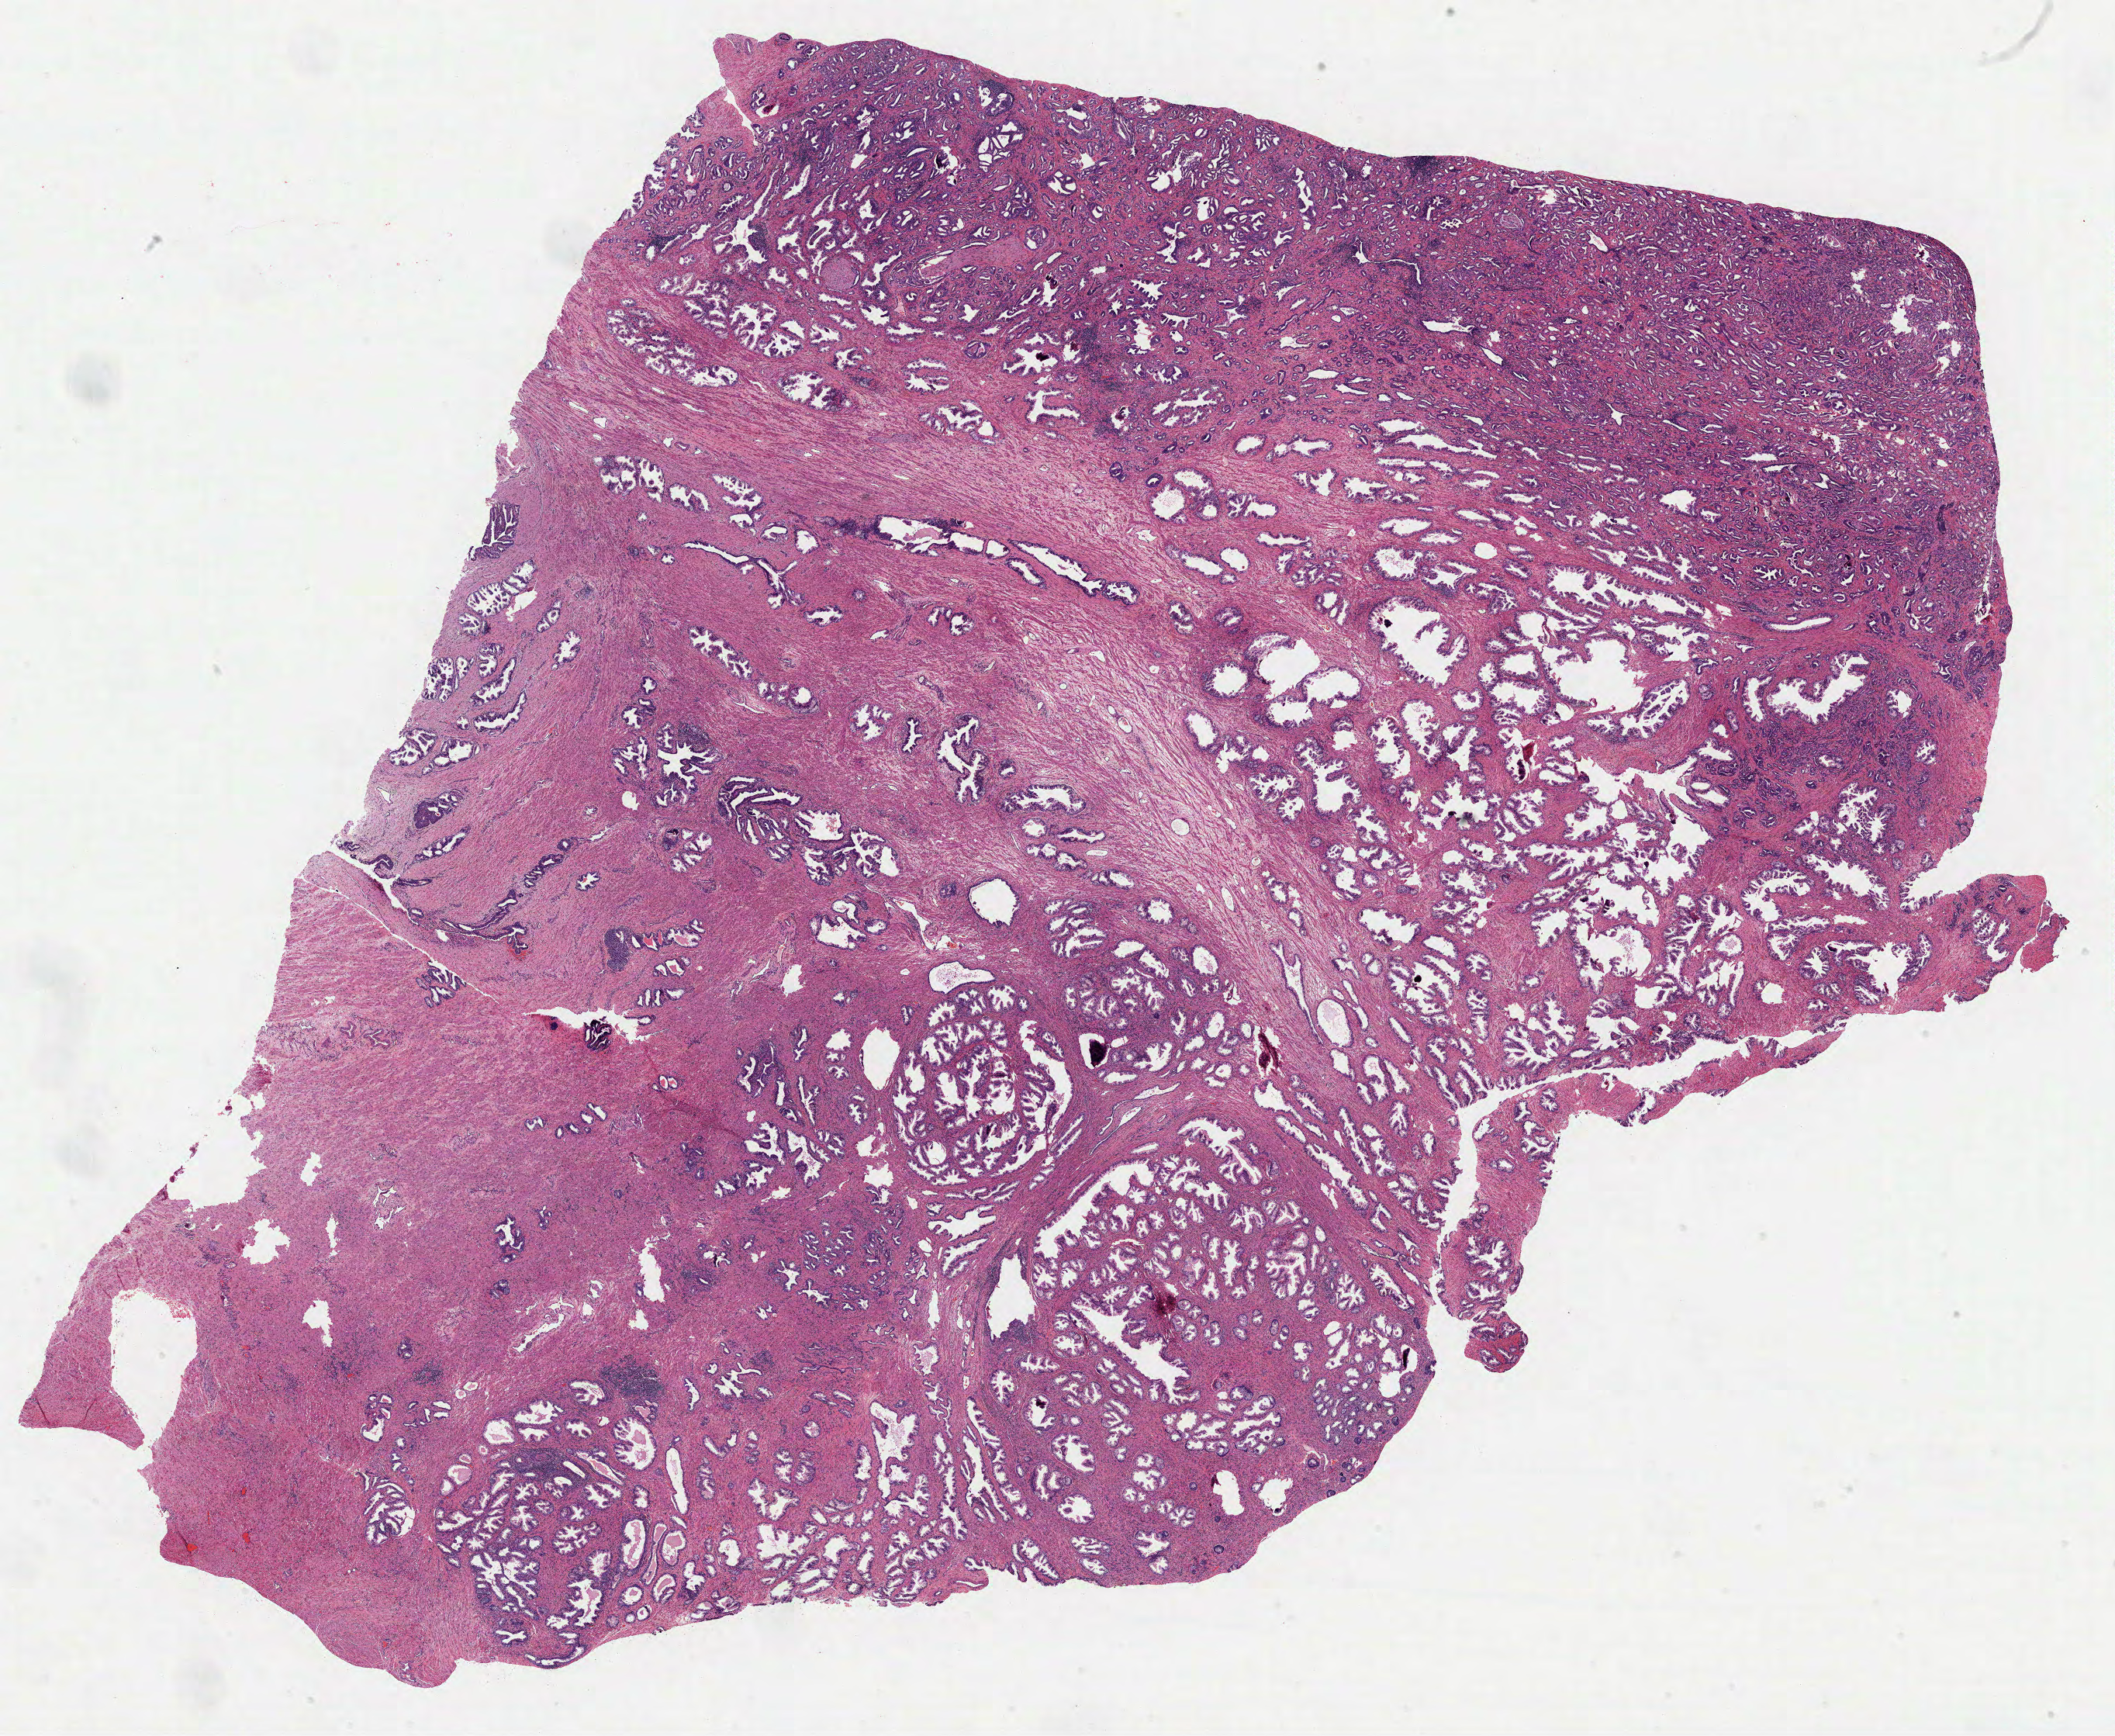
H&E whole-slide image — shown as a low-resolution overview of the whole scanned area (about 22.0 x 18.1 mm, acquisition: 40x scan); formalin-fixed paraffin-embedded (FFPE) diagnostic section; sample: primary tumour, prostate. Patient: male, age at initial diagnosis 57 years. Gleason score: 6 (3+3).
- lymph nodes positive (case pathology): 0 of 25 examined
- laterality: bilateral
- histologic diagnosis: Acinar cell carcinoma (prostate gland)